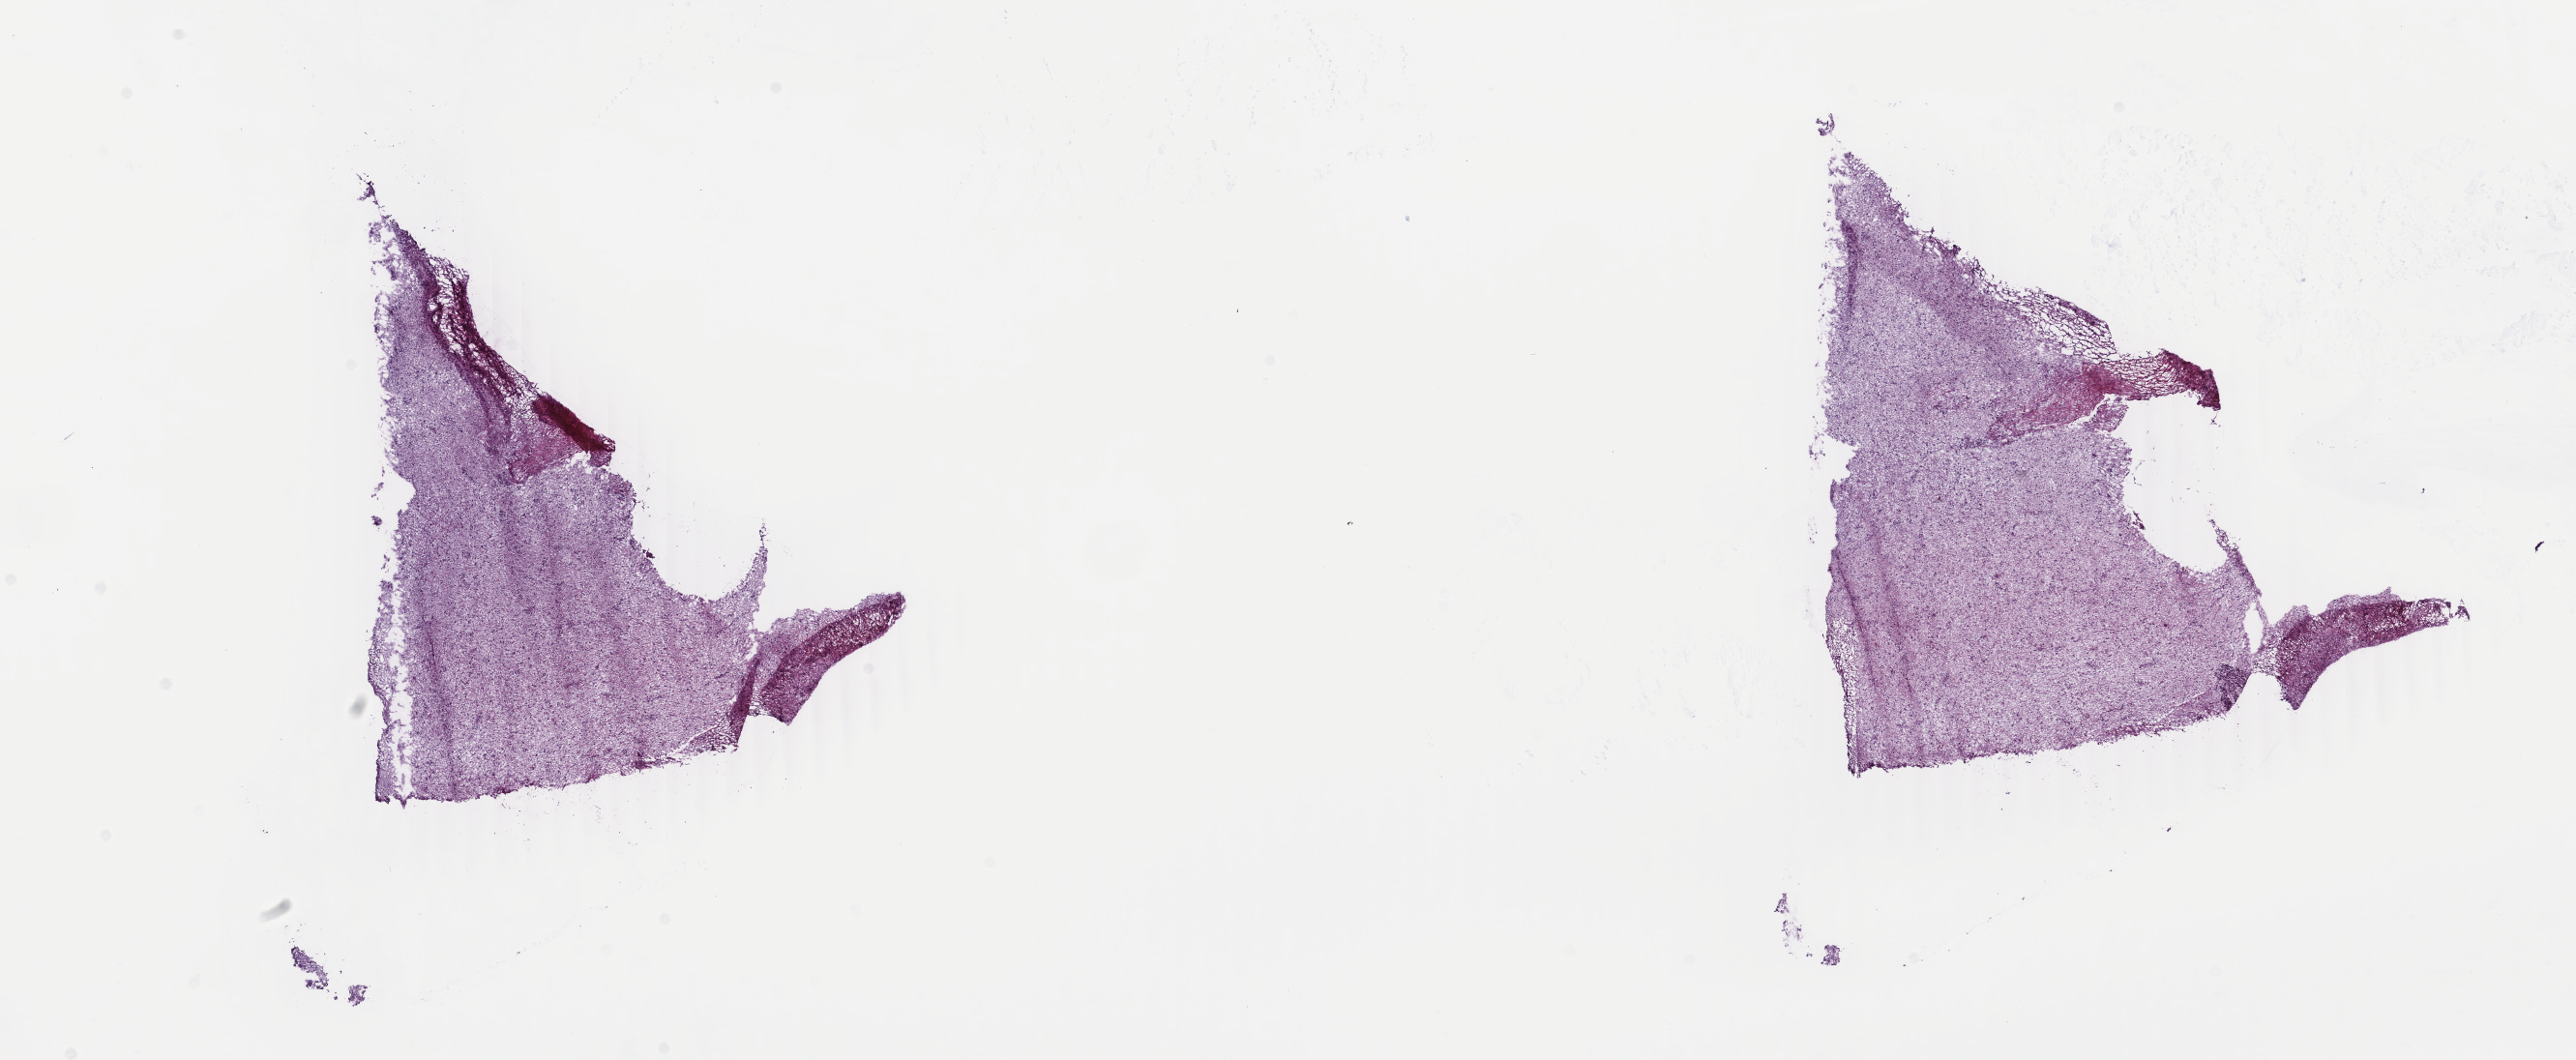
Hematoxylin and eosin (H&E) stained whole-slide image, low-resolution overview of the scanned area, about 21.2 x 8.7 mm (slide scanned at 40x); frozen section from the top of the tissue portion; brain, primary tumour sample. Female patient; age at initial diagnosis 37 years. Histologic grade: G2 (moderately differentiated). Pathologist review of this section (percent, as recorded): tumour cells 30%, tumour nuclei 80%, normal cells 10%, stromal cells 60%, necrosis 0%. Inflammatory infiltration, as recorded: lymphocyte infiltration 0%, monocyte infiltration 0%, neutrophil infiltration 0%.
Histologic diagnosis: Astrocytoma, NOS (cerebrum).